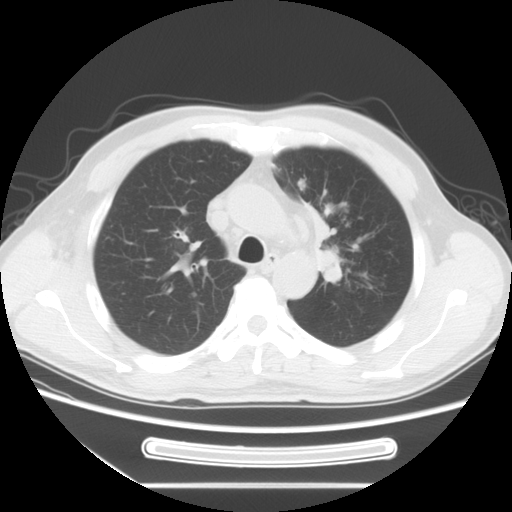
Chest CT, one axial slice. Position 51 of 71 along the scan axis. Reconstruction kernel STANDARD. 120 kVp. Lung window (W 1500 / L -600 HU). 5 mm slice thickness. 512 × 512 image matrix, field of view 366 × 366 mm. Male patient, age 51 years. Case-level facts recorded for this patient, not image findings: clinical TNM (as recorded): T1c N3 M0.
Annotated regions visible in this slice (rectangle marked by the reading radiologist):
- lung tumour (recorded histology: adenocarcinoma): bounding box (x1, y1, x2, y2) in pixels: (304, 194, 363, 289)